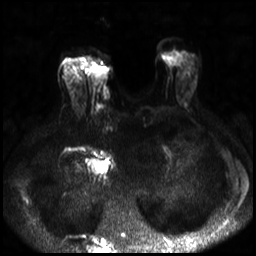
Breast MRI, one axial slice; slice 9 of 30 in the series (ordered by position); diffusion-weighted series; image 2 of 4 stored at this slice position (different b-values; order by instance number); 3 T; 4 mm slice thickness; 256 × 256 image matrix, field of view 320 × 320 mm. Female patient.
Structures marked on this image (expert manual segmentation):
- tumour on diffusion-weighted imaging: box from (x=91, y=66) to (x=108, y=83) px